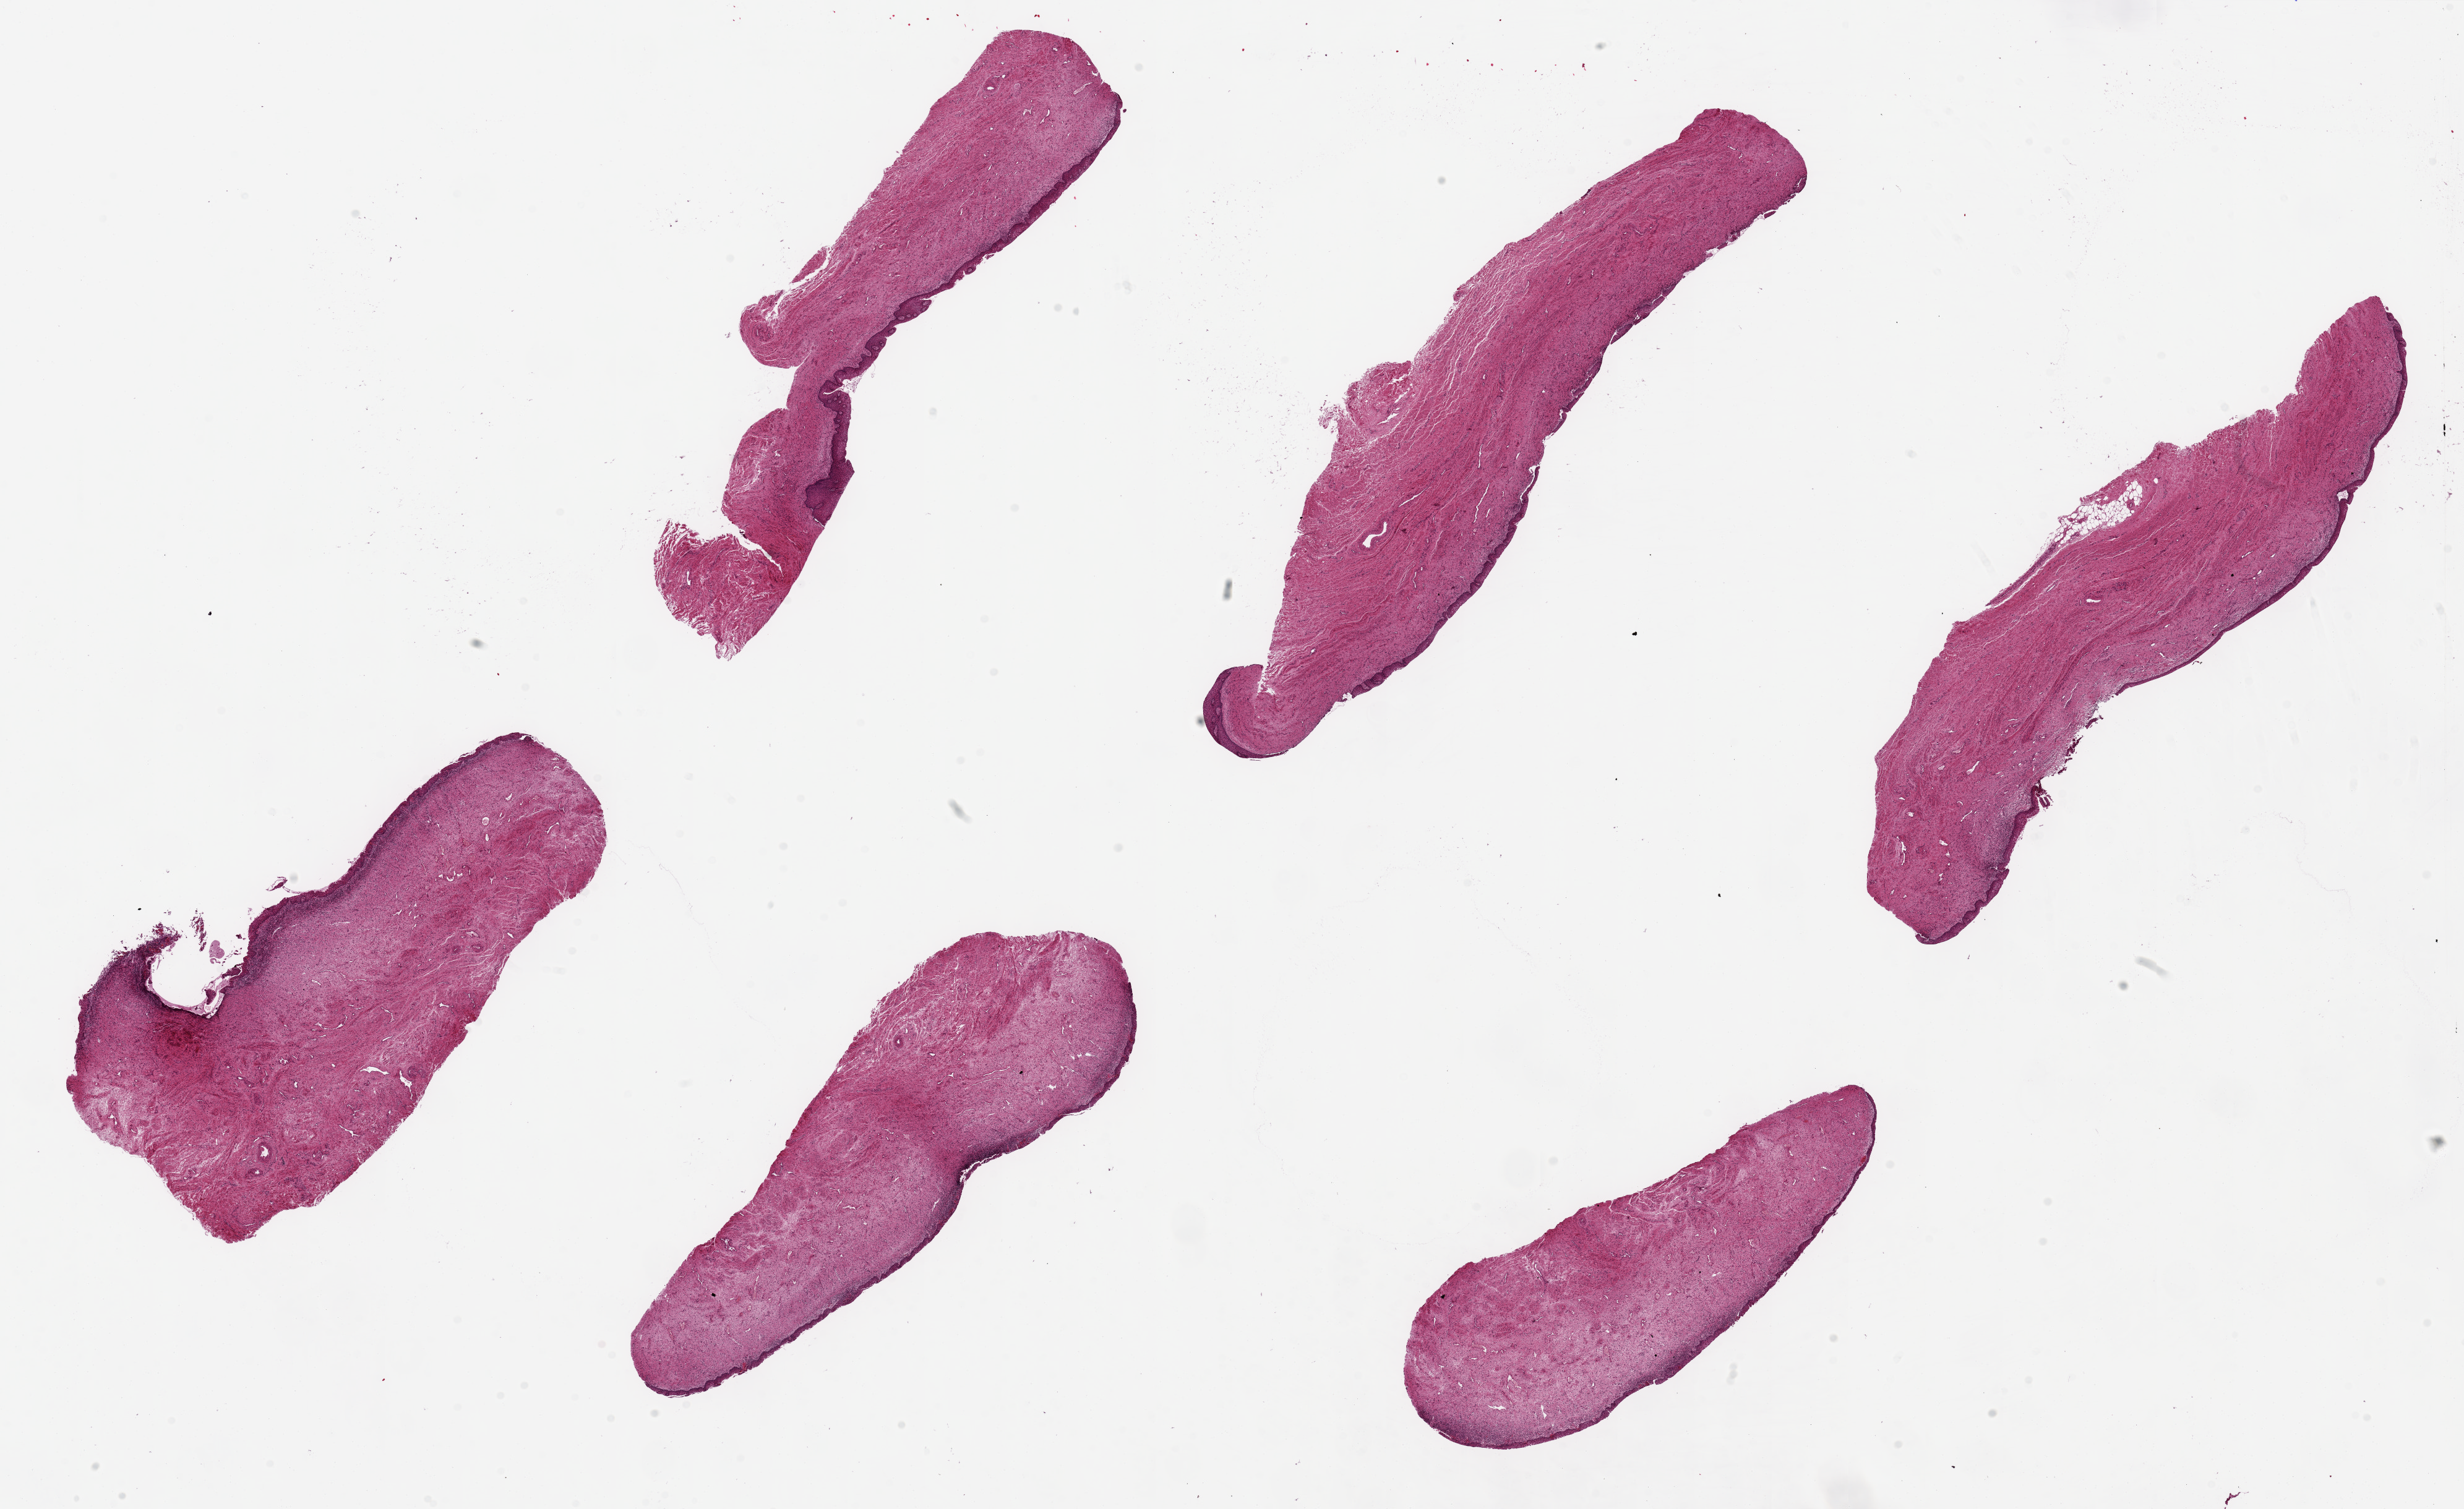
H&E whole-slide image — low-resolution overview of the scanned area, about 31.5 x 19.3 mm; PAXgene-fixed, paraffin-embedded tissue; target tissue: vagina; donor tissue sample.
• pathologist's review note for this sample: 6 pieces, up to 11x3mm; 1% sloughing squamous mucosa